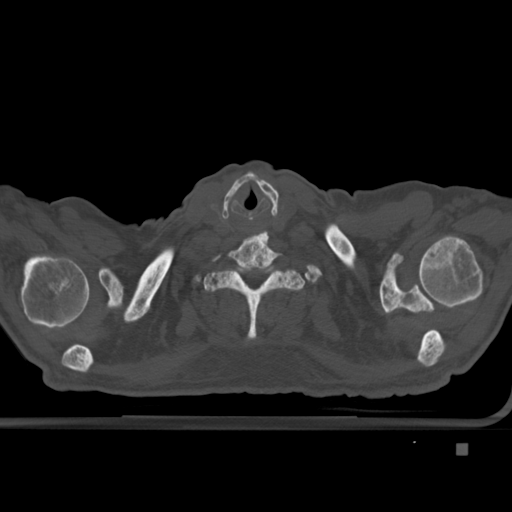
CT including the spine, one axial slice; slice 363 of 451 in the series (ordered by position); bone window (W 1800 / L 400 HU); 1.5 mm slice thickness; 512 × 512 image matrix, field of view 378 × 378 mm. Patient: male, 75 years. From the clinical record (not read from this slice): primary cancer: prostate.
Annotated regions visible in this slice (semi-automatically segmented with operator editing):
- T1 vertebra: bounding box (x1, y1, x2, y2) in pixels: (203, 262, 305, 339)